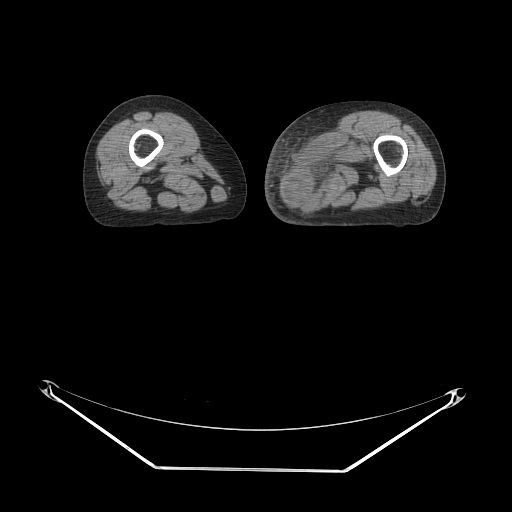
CT of an extremity soft-tissue mass (from a PET/CT study), one axial slice; position 18 of 91 along the scan axis; reconstruction kernel STANDARD; soft-tissue window (W 400 / L 40 HU); 512 × 512 image matrix. Female patient. From the clinical record (not read from this slice): histological type: pleomorphic leiomyosarcoma; grade: high; site of the primary tumour: left thigh.
Structures marked on this image (expert contour drawn on MRI and transferred to this co-registered scan by the dataset authors):
- gross tumour volume including surrounding oedema: bounding box [x1, y1, x2, y2] px = [285, 130, 373, 206]
- gross tumour volume (mass): [285, 160, 327, 204]